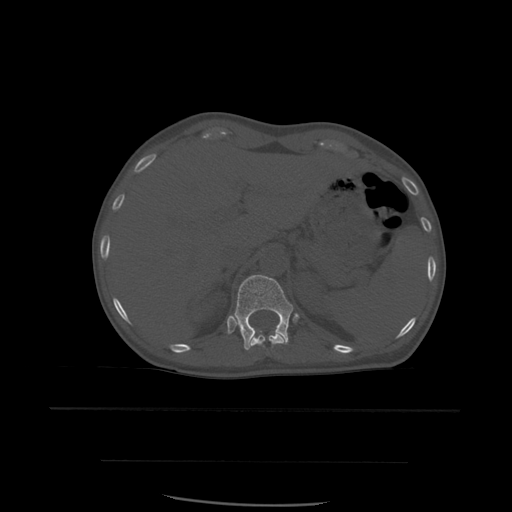
CT including the spine, one axial slice. Position 281 of 574 along the scan axis. Bone window (W 1800 / L 400 HU). 1.25 mm slice thickness. 512 × 512 image matrix, field of view 392 × 392 mm. Patient age 48 years. Case-level facts recorded for this patient, not image findings: primary cancer: lung; vertebrae with lytic lesions (as recorded): T11.
Outlined on this slice (semi-automatic segmentation, software-assisted and operator-edited):
- T11 vertebra: bounding box <249,333,285,348> (left, top, right, bottom; pixels)
- T12 vertebra: <235,275,294,350>